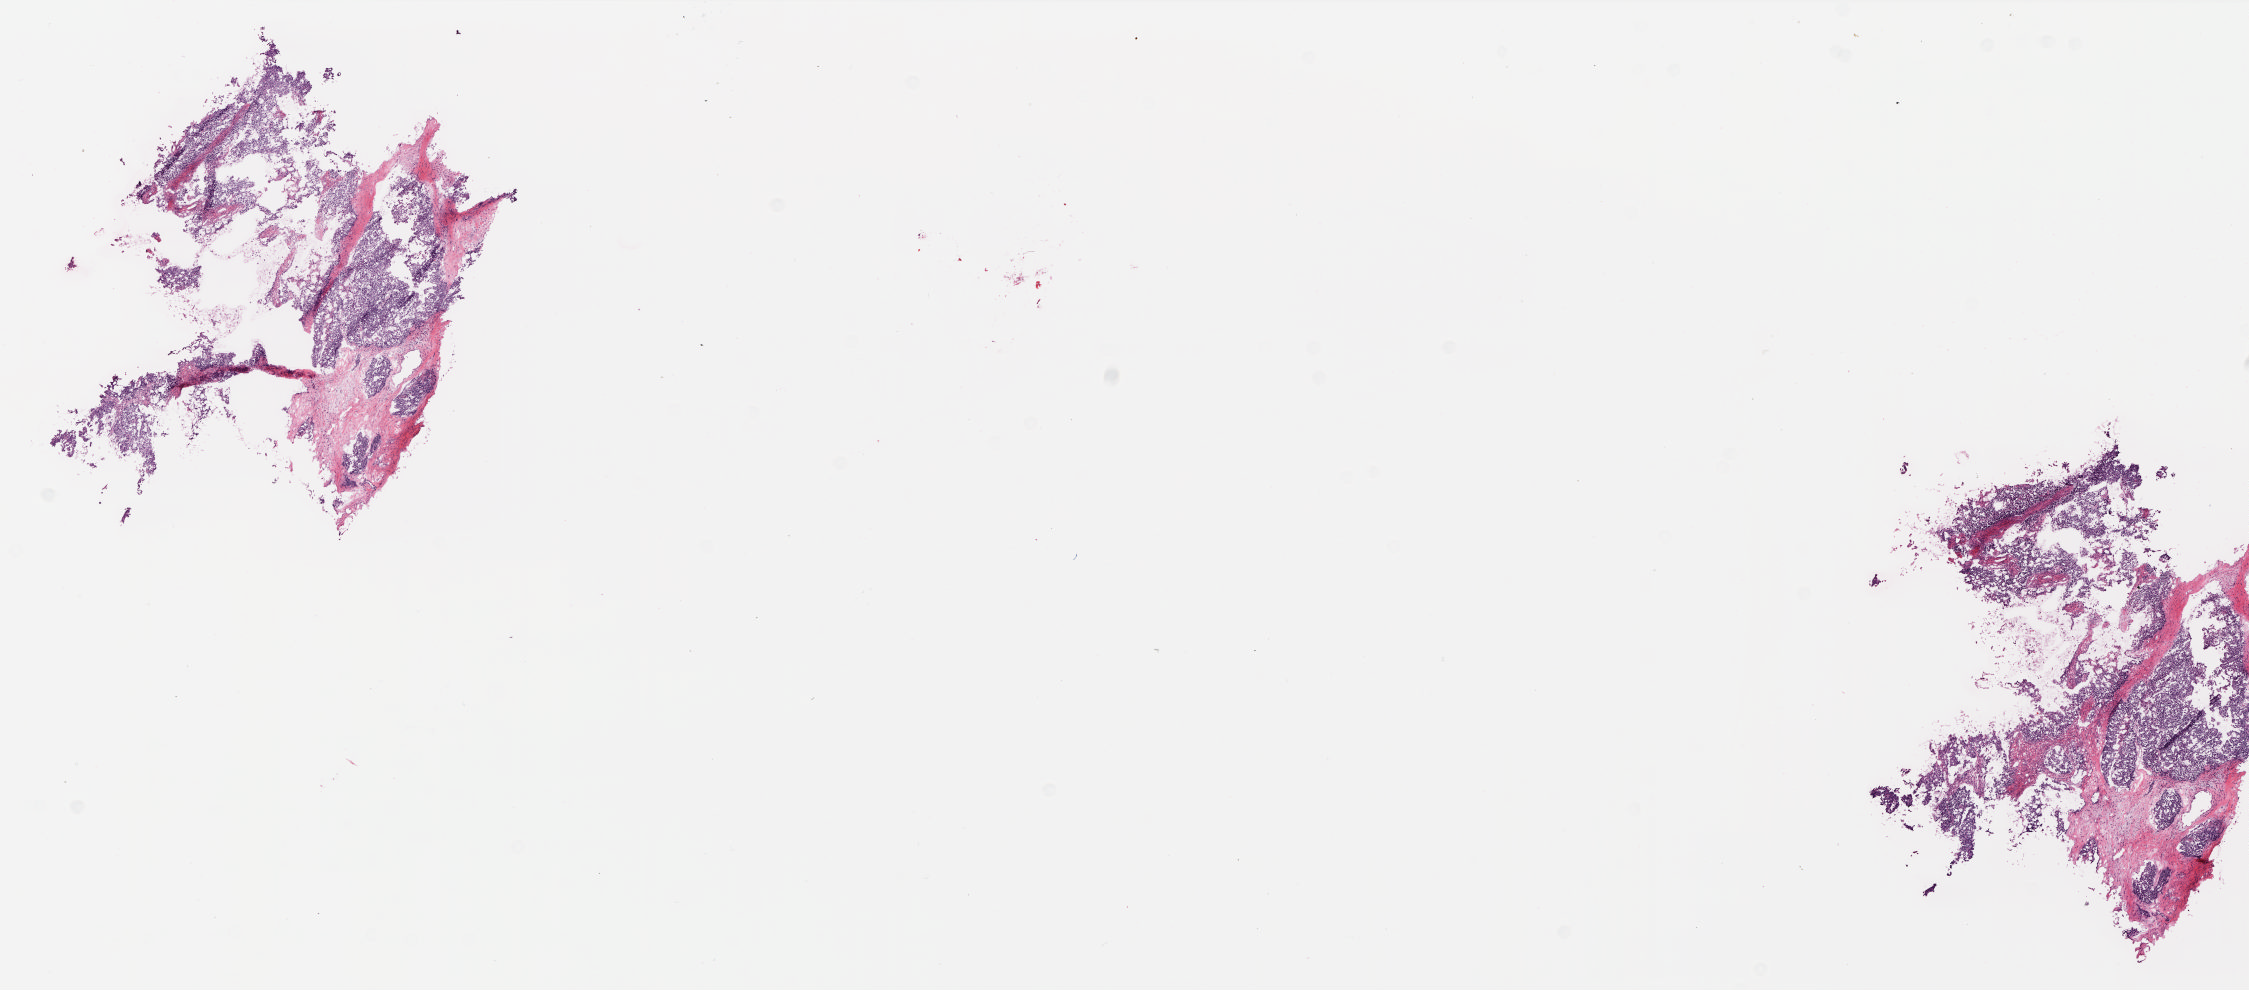
H&E whole-slide image — a low-resolution overview of the entire scanned area, about 18.0 x 7.9 mm (from a 20x scan). Frozen section. Ovary, primary tumour sample. Patient: female, age at initial diagnosis 58 years. Histologic grade: G3 (poorly differentiated). Slide review estimates, as recorded: tumour cells 80%, tumour nuclei 90%, normal cells 0%, stromal cells 15%, necrosis 5%.
Pathologic diagnosis: Serous cystadenocarcinoma, NOS. Laterality: bilateral. FIGO stage: IIIC.